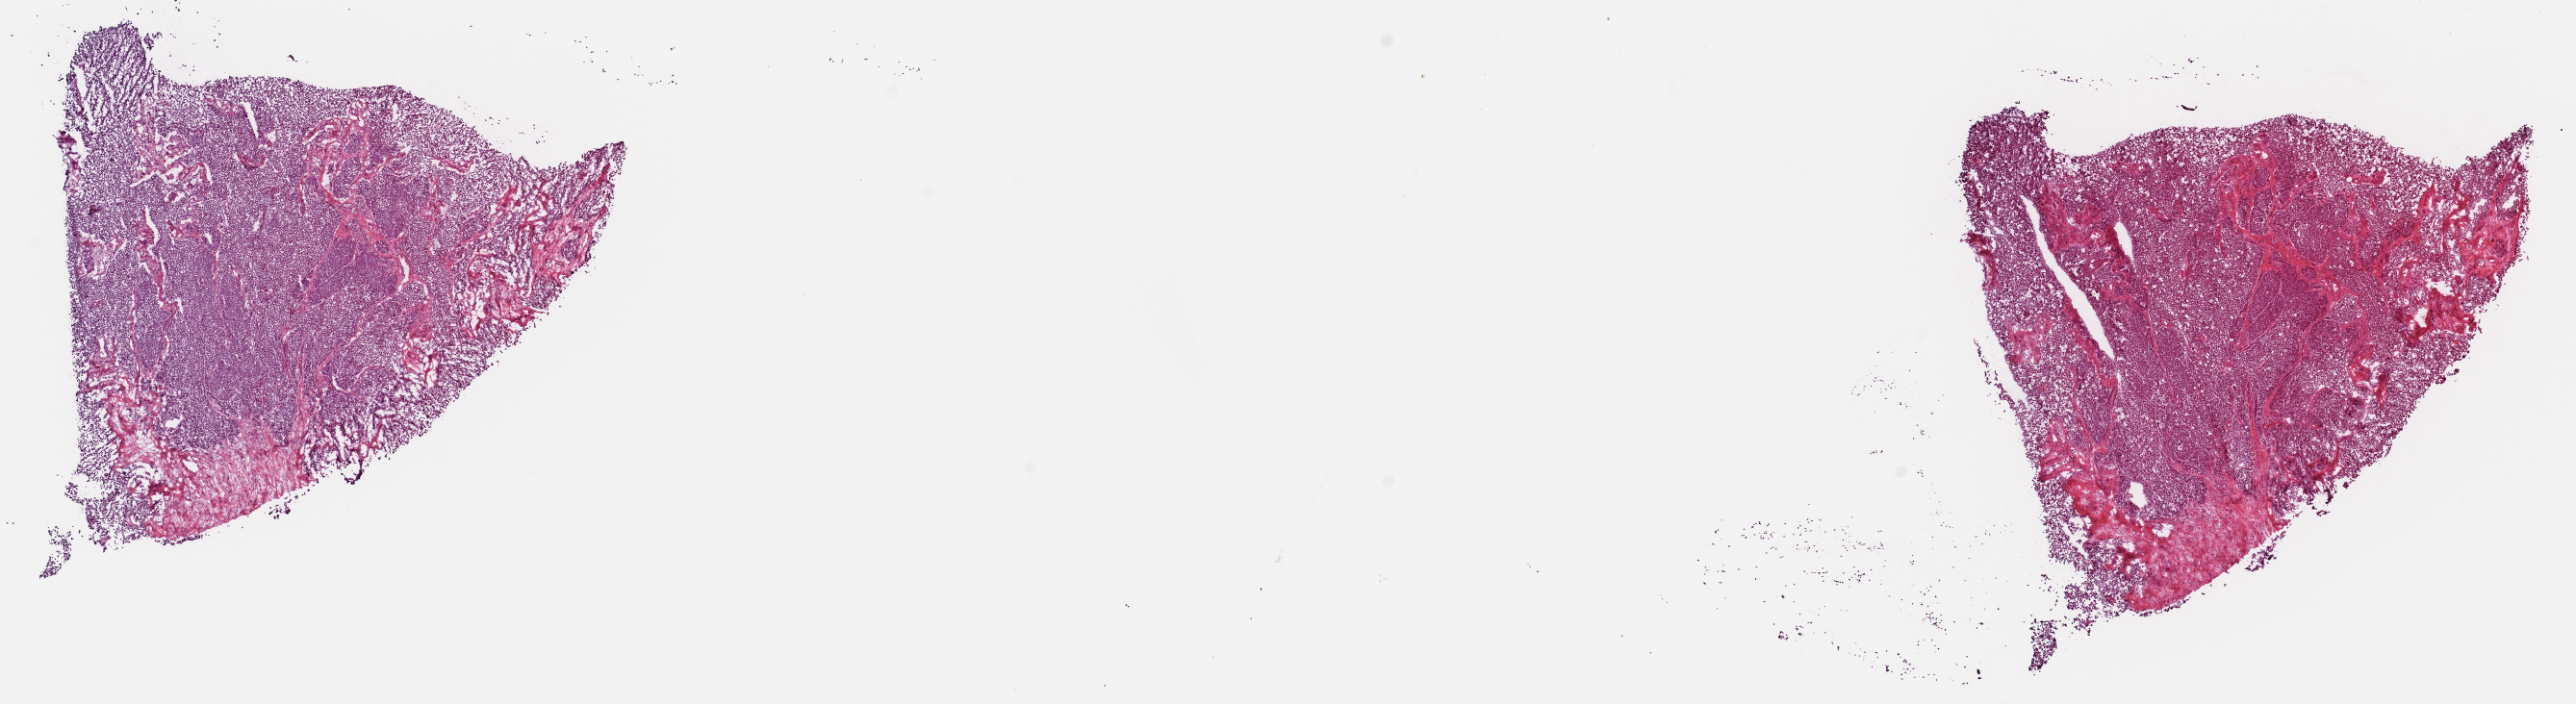
Digitized H&E tissue section (whole slide), whole scanned area (about 21.1 x 5.8 mm, acquisition: 40x scan) shown as a low-resolution overview; frozen section from the top of the tissue portion; primary tumour sample from the skin. Female patient; age at initial diagnosis 49 years. Composition of this section per pathologist review: tumour cells 90%, tumour nuclei 90%, normal cells 0%, stromal cells 10%, necrosis 0%. Infiltration values recorded for this section: lymphocyte infiltration 1%, monocyte infiltration 0%, neutrophil infiltration 0%.
Histologic diagnosis: Malignant melanoma, NOS. AJCC pathologic stage: IIC (6th edition). TNM: T4b N0 M0.